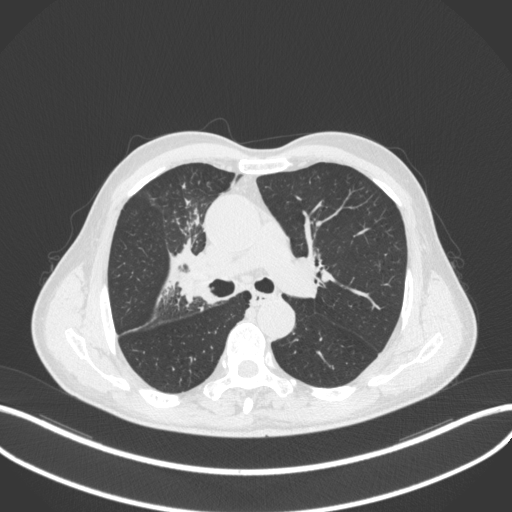
Chest CT, one axial slice; position 306 of 490 along the scan axis; reconstruction kernel B31f; lung window (W 1500 / L -600 HU); 1 mm slice thickness; 512 × 512 image matrix, field of view 400 × 400 mm. Male patient, age 69 years. From the clinical record (not read from this slice): clinical TNM (as recorded): T2a N0 M0.
Outlined on this slice (rectangle marked by the reading radiologist):
- lung tumour (recorded histology: adenocarcinoma): box from (x=171, y=266) to (x=204, y=305) px